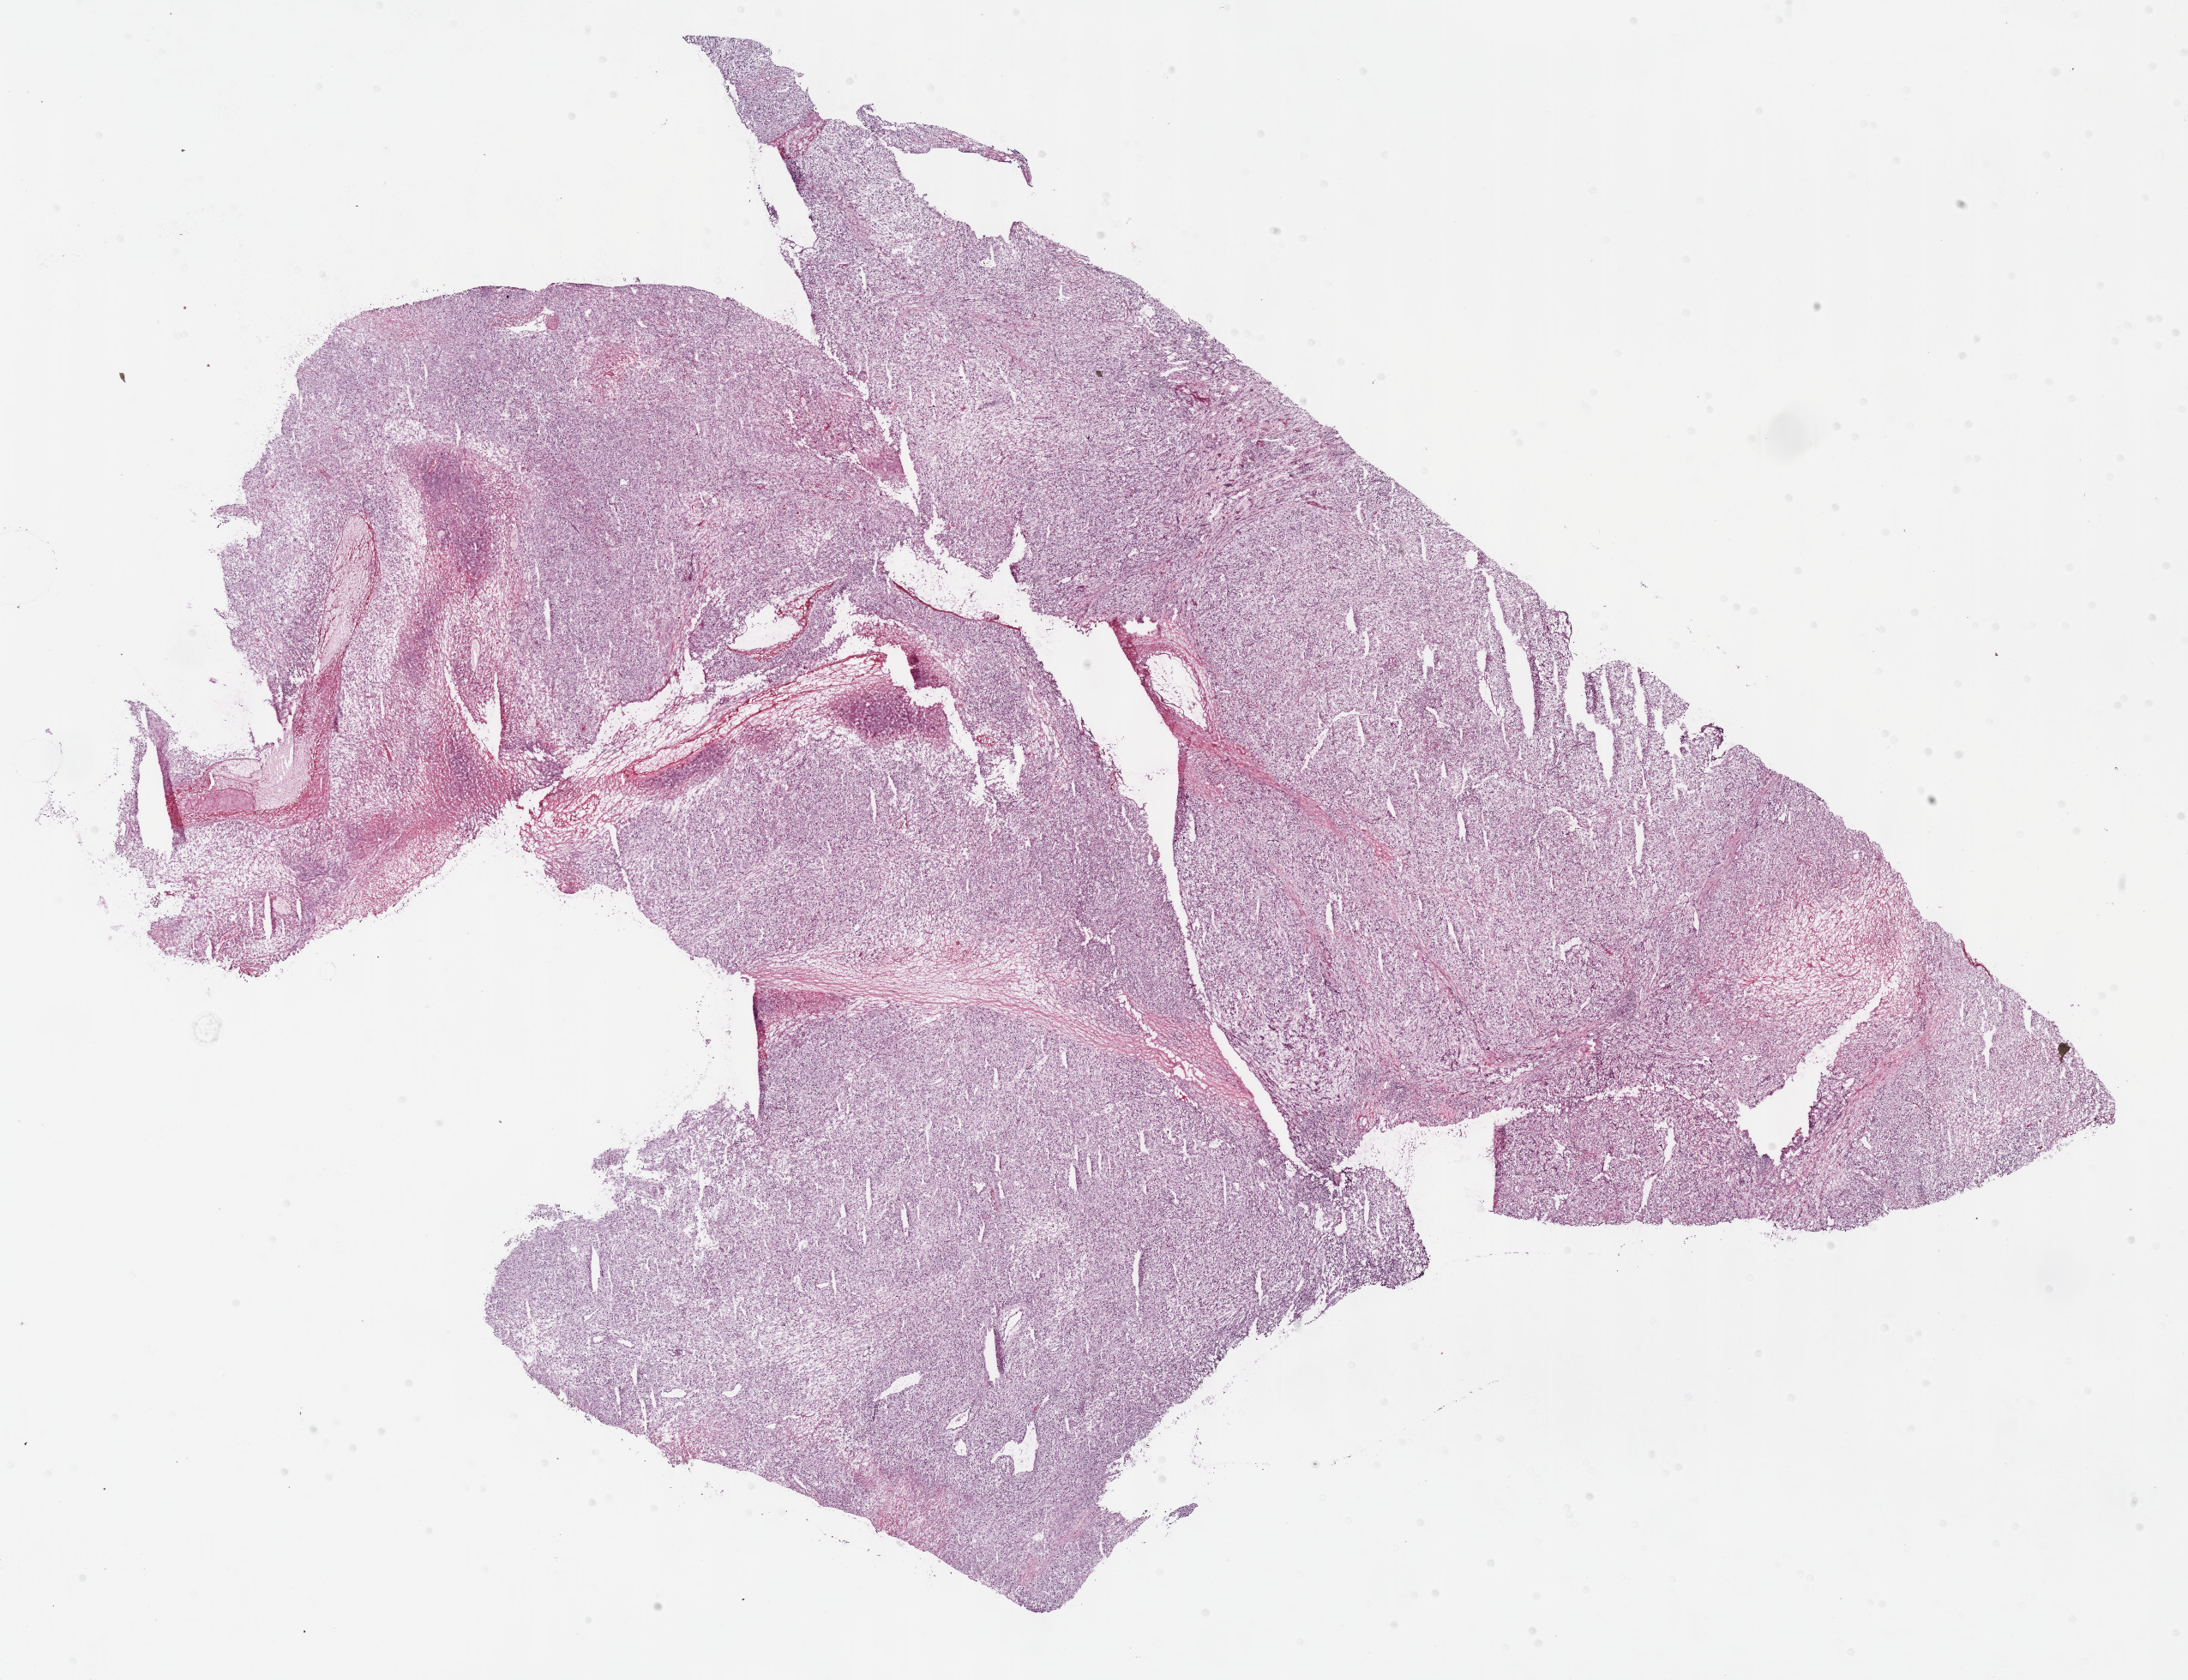
Hematoxylin and eosin (H&E) stained whole-slide image — low-resolution overview of the scanned area, about 20.6 x 15.9 mm (acquisition: 40x scan); frozen section from the bottom of the tissue portion; sample: primary tumour, kidney. Male patient; age at initial diagnosis 65 years. Histologic grade: G3 (poorly differentiated). Composition of this section per pathologist review: tumour cells 79%, tumour nuclei 80%, normal cells 1%, stromal cells 10%, necrosis 10%.
AJCC pathologic stage: IV. Laterality: right. TNM: T4 N0 M1. Diagnosis: Clear cell adenocarcinoma, NOS.